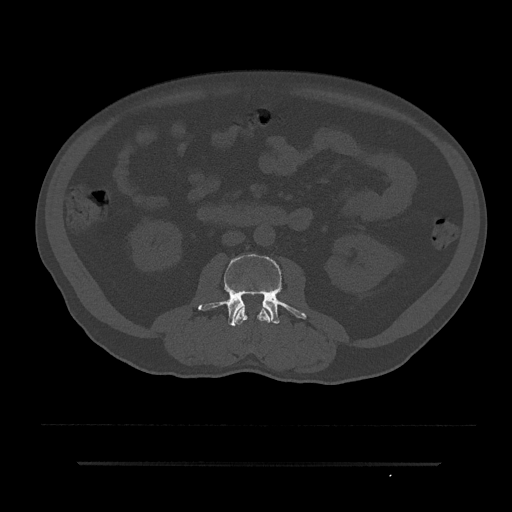
CT including the spine, one axial slice. Position 25 of 797 along the scan axis. Reconstruction kernel Br40s/3. 120 kVp. Bone window (W 1800 / L 400 HU). 0.5 mm slice thickness. 512 × 512 image matrix. Patient: male, 59 years. From the clinical record (not read from this slice): primary cancer: bile ducts.
Annotated regions visible in this slice (semi-automatic segmentation, software-assisted and operator-edited):
- L2 vertebra: bounding box (x1, y1, x2, y2) in pixels: (233, 305, 273, 325)
- L3 vertebra: (198, 254, 307, 326)